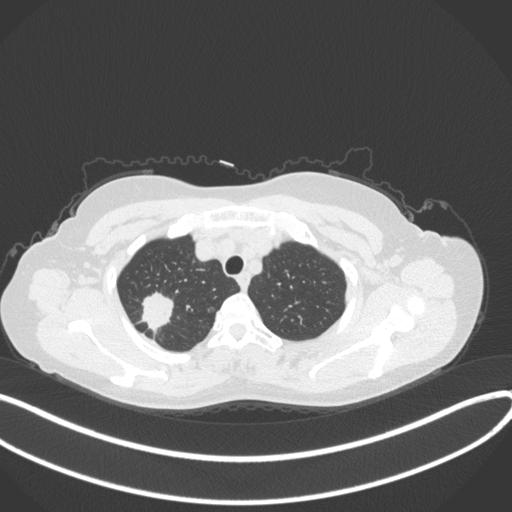
Chest CT, one axial slice; position 308 of 342 along the scan axis; reconstruction kernel B31f; lung window (W 1500 / L -600 HU); 512 × 512 image matrix, field of view 400 × 400 mm. Patient: female, 50 years. From the clinical record (not read from this slice): clinical TNM (as recorded): T1c N0 M0.
Annotated regions visible in this slice (bounding box drawn by a radiologist):
- lung tumour (recorded histology: adenocarcinoma): bounding box [x1, y1, x2, y2] px = [137, 289, 179, 335]